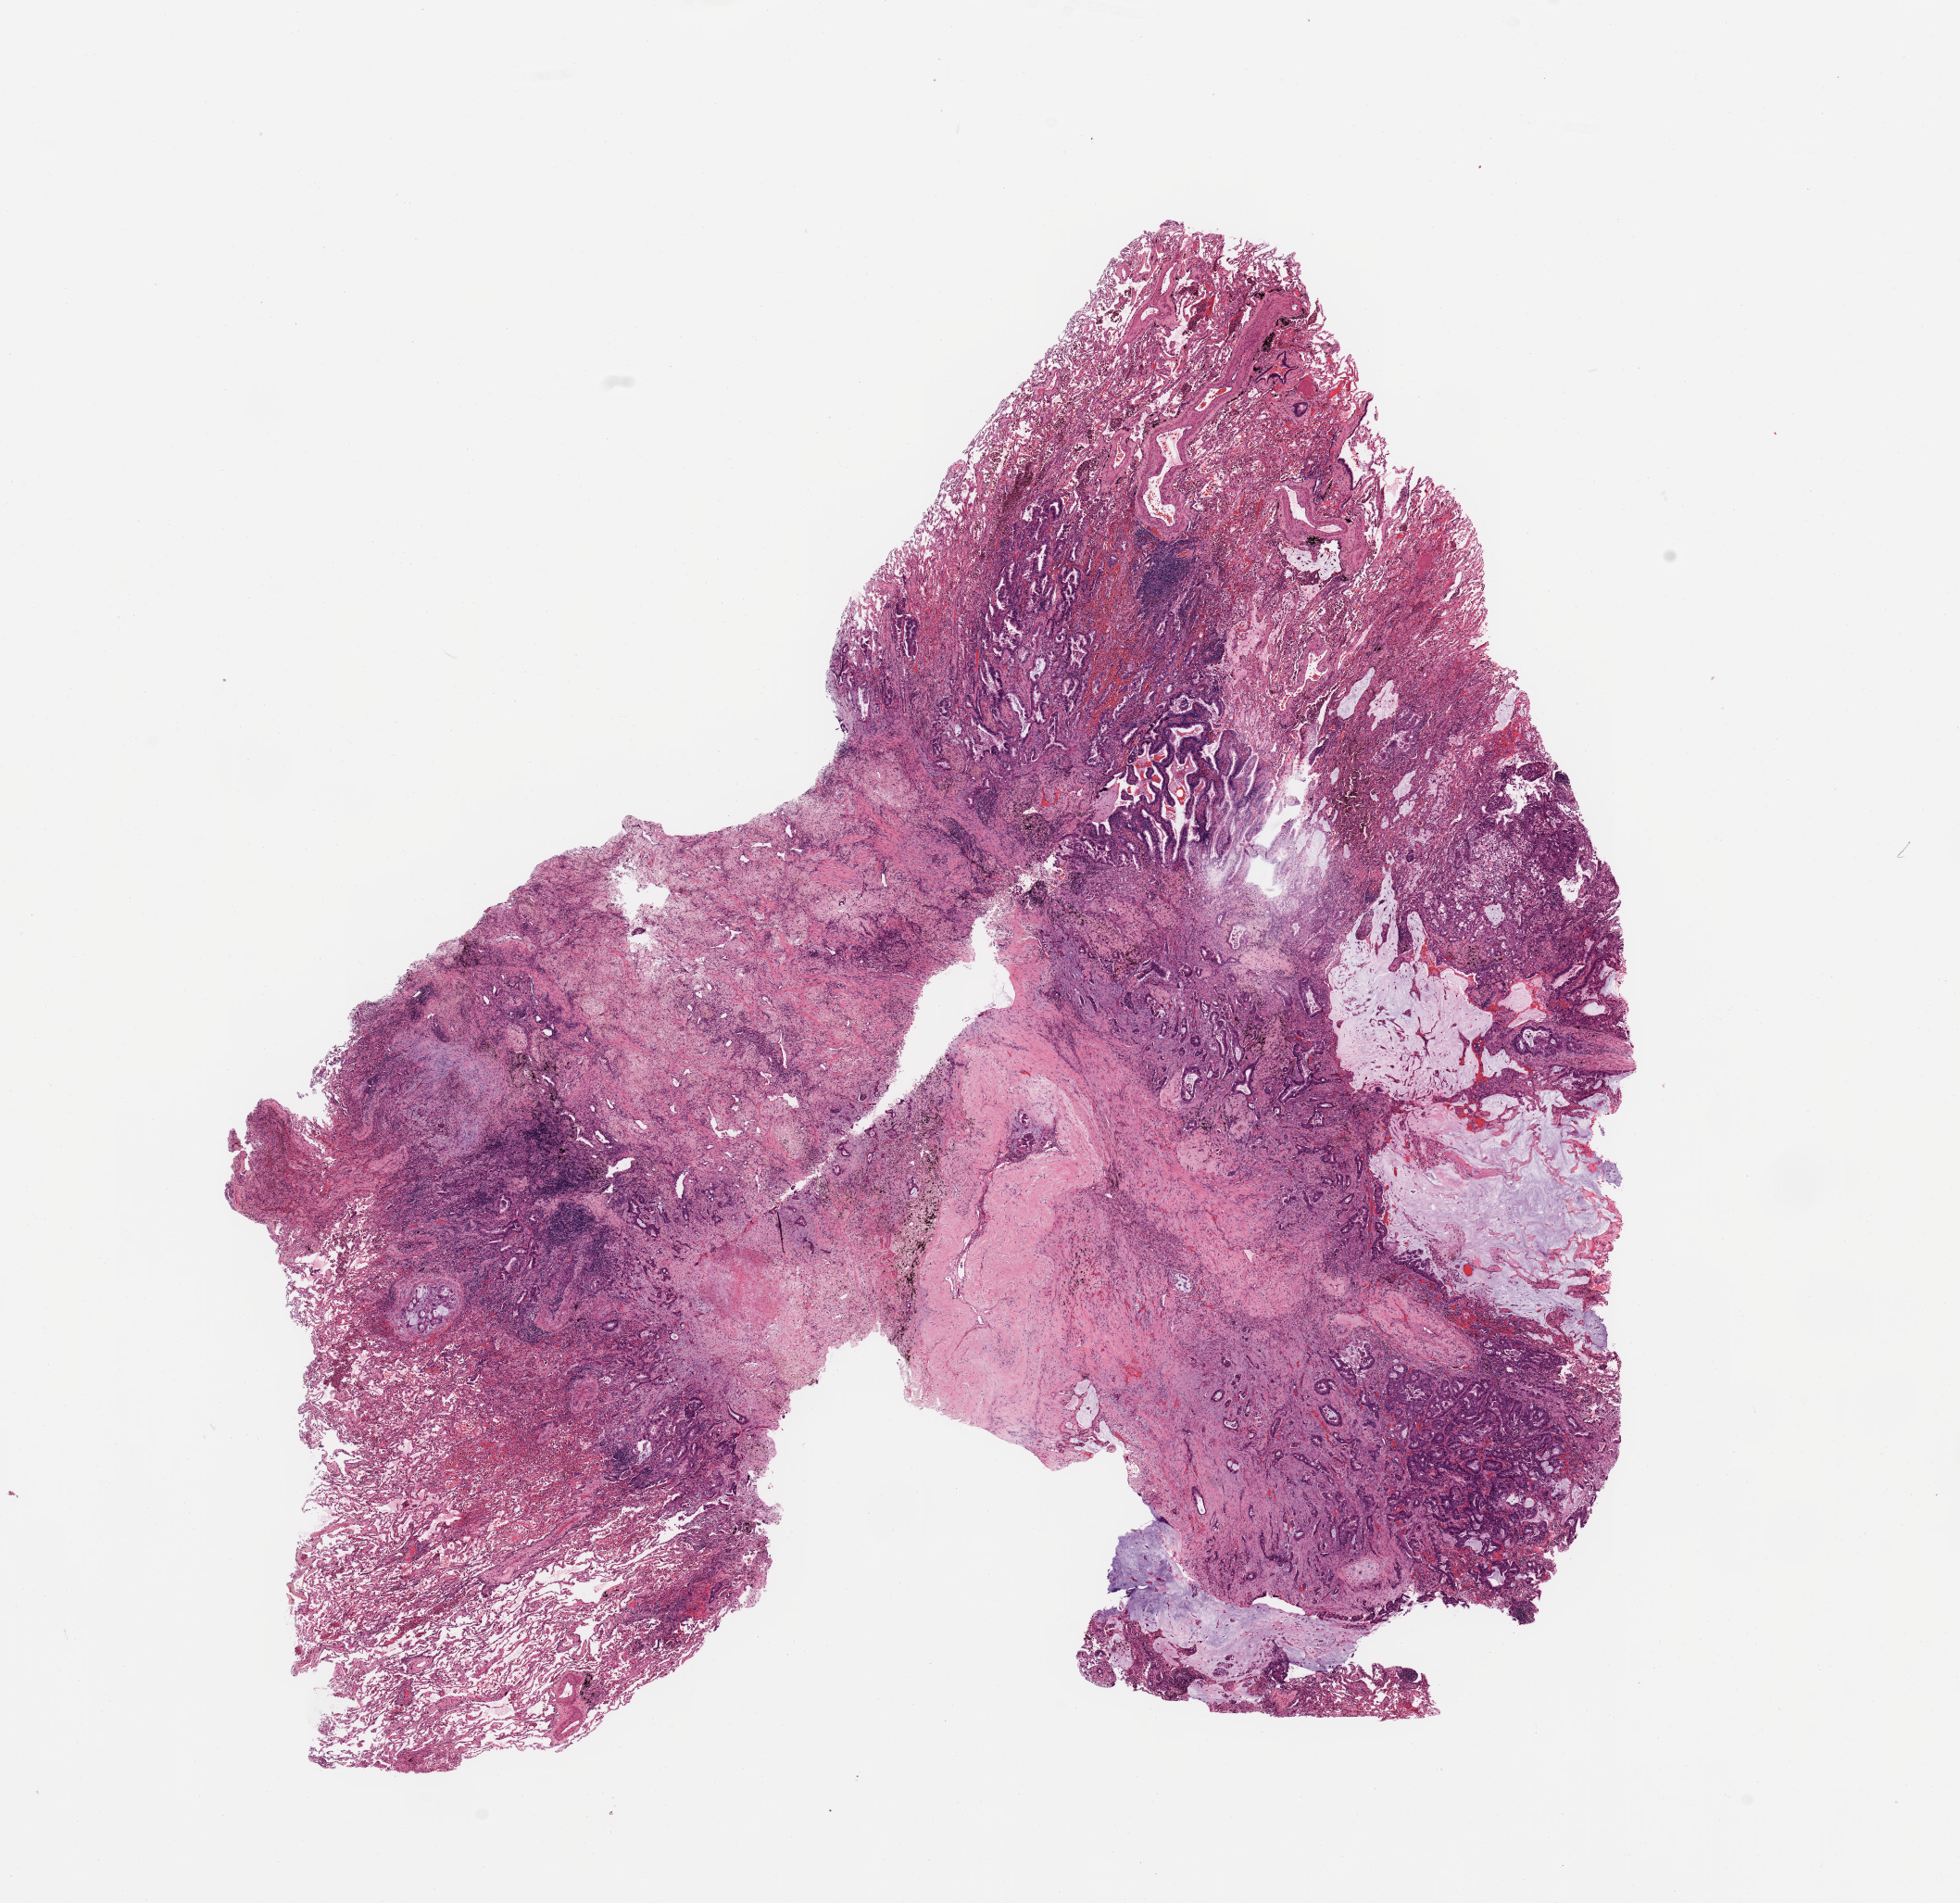
Whole-slide histology image, Hematoxylin and eosin (H&E) stained, low-resolution overview of the scanned area, about 16.7 x 16.2 mm; tumour tissue sample, sampled site: lung. Male, 64 y/o. Histologic grade: G2 (moderately differentiated). Pathologist review of this section (percent, as recorded): tumour nuclei 60%, necrosis 5%.
AJCC pathologic stage: IIIA. Histologic diagnosis: Adenocarcinoma, NOS. Primary tumour site (as recorded): right upper lobe.